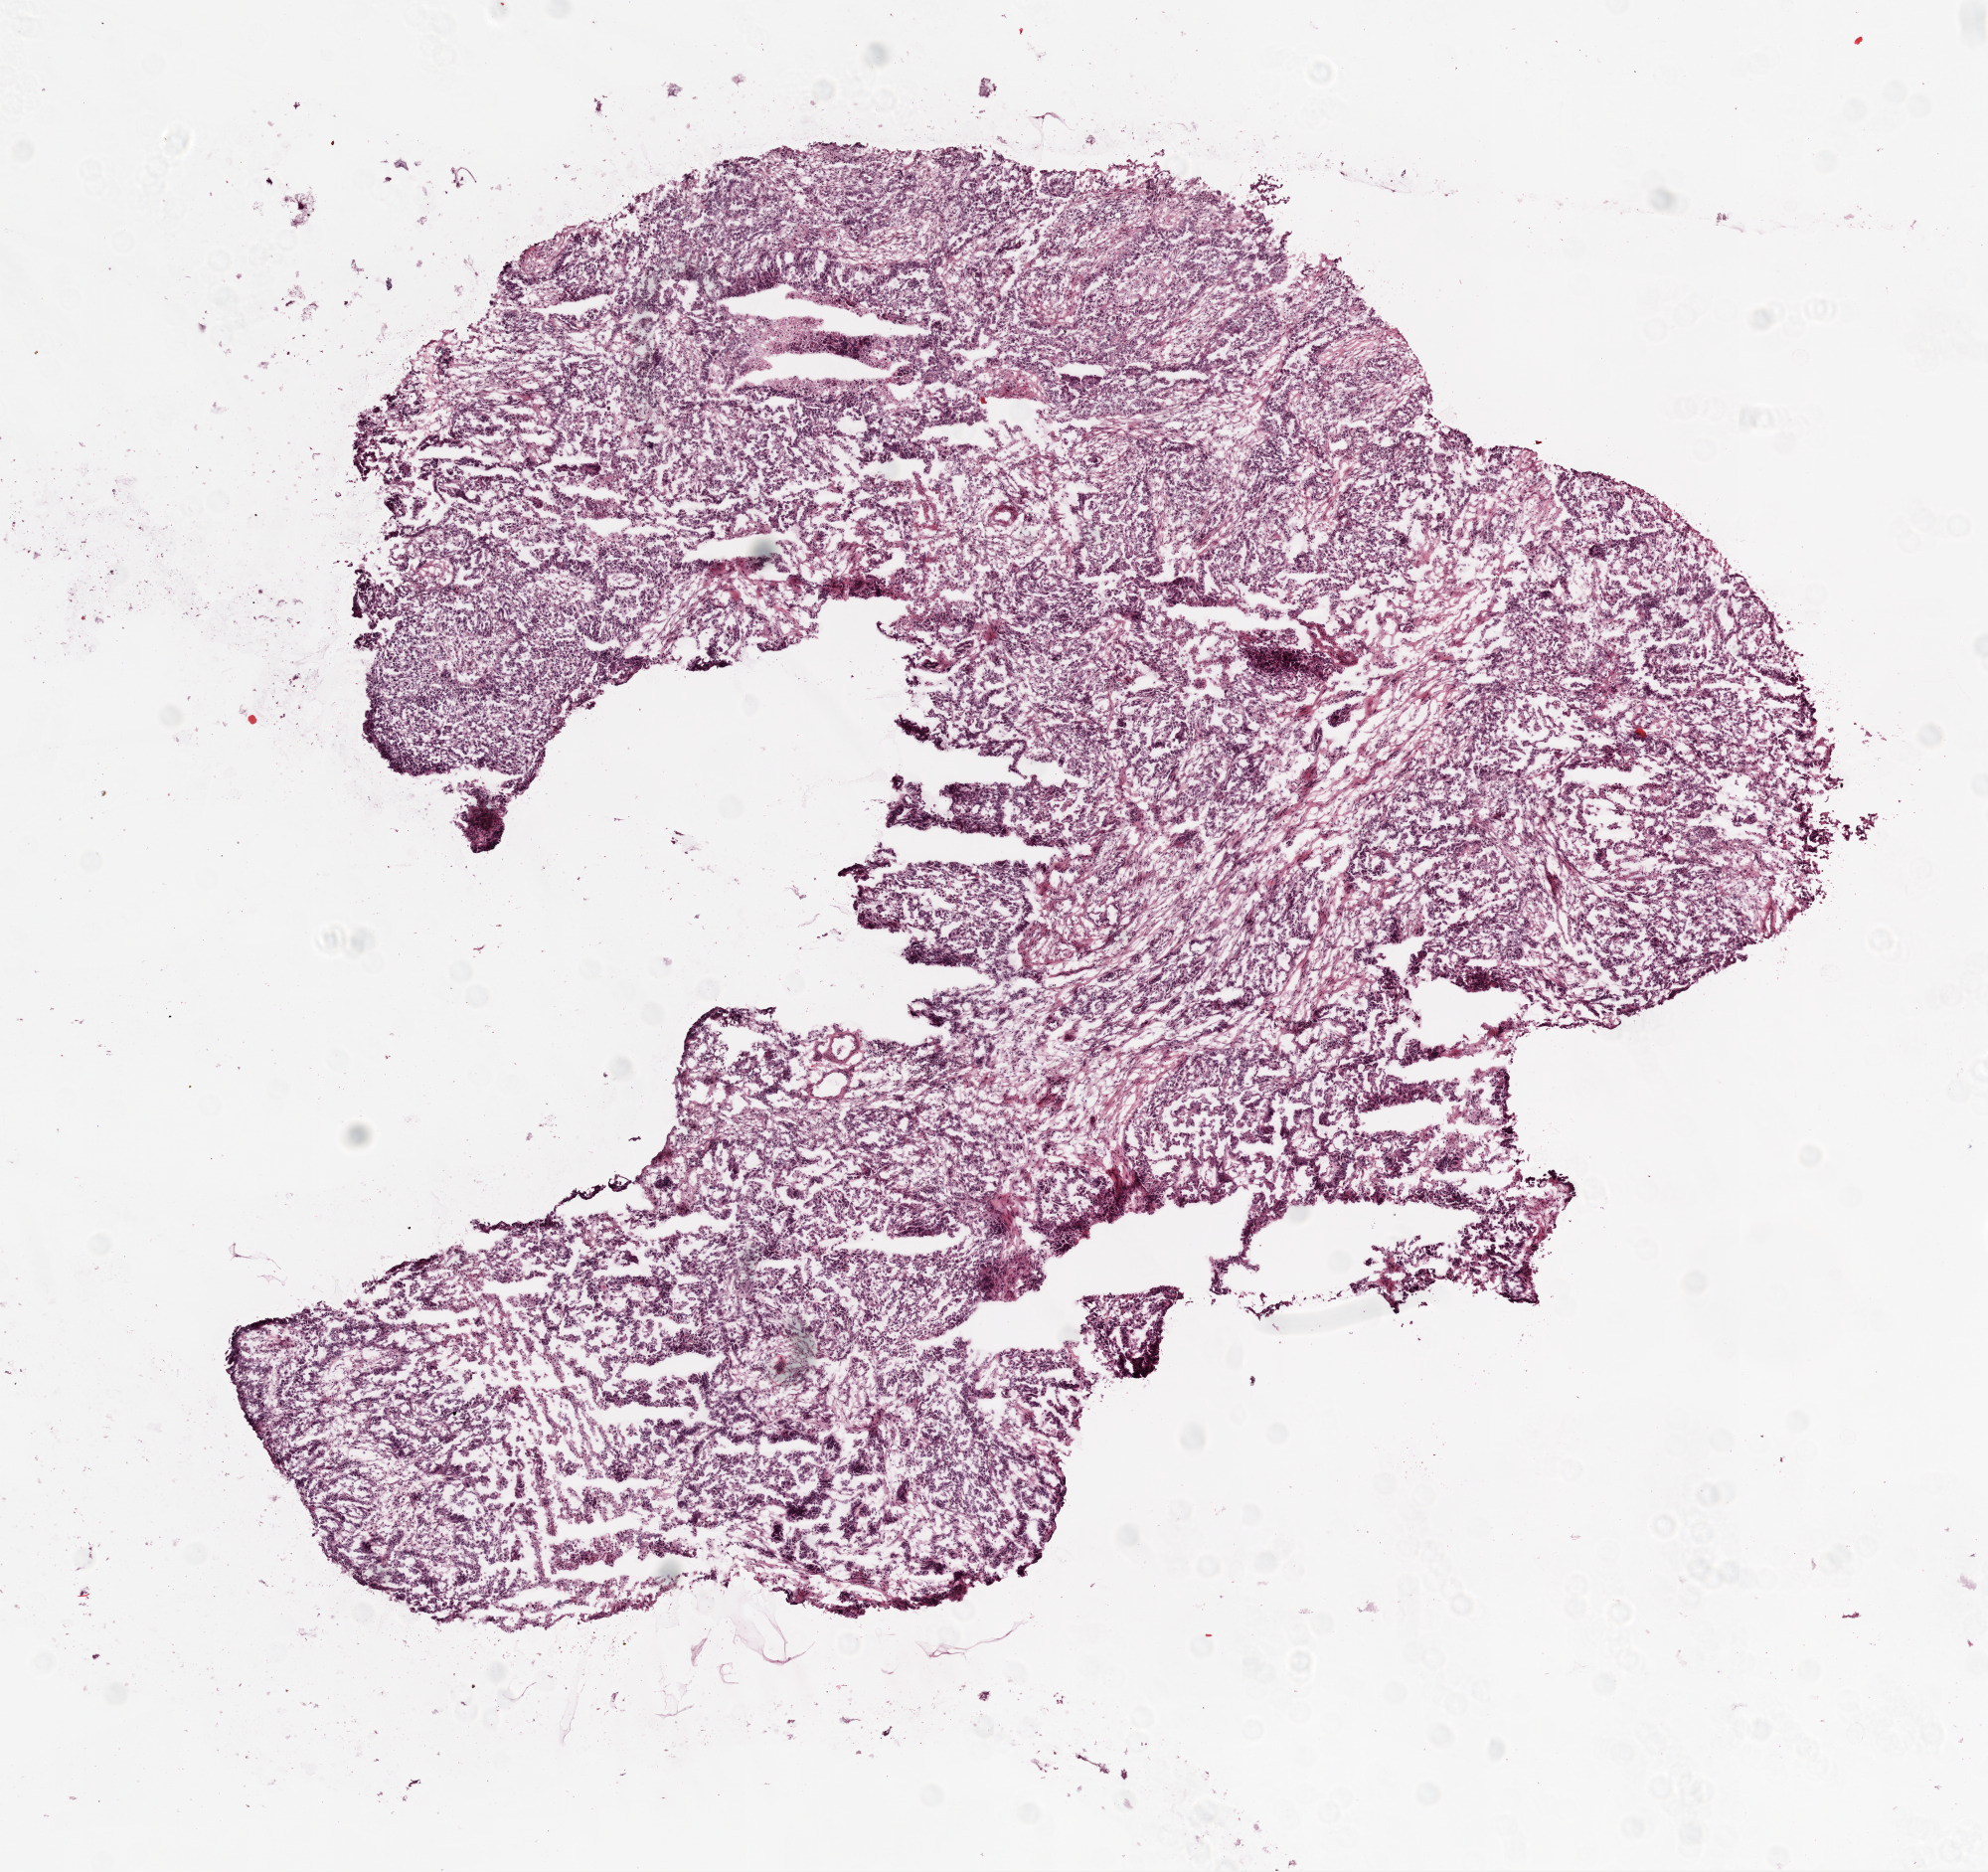
H&E-stained whole-slide image, whole scanned area (about 8.0 x 7.6 mm, acquisition: 20x scan) shown as a low-resolution overview; frozen section from the top of the tissue portion; ovary, primary tumour sample. Female patient; age at initial diagnosis 49 years. Histologic grade: G2 (moderately differentiated). Composition of this section per pathologist review: tumour cells 85%, tumour nuclei 85%, normal cells 0%, stromal cells 12%, necrosis 3%. Inflammatory infiltration, as recorded: lymphocyte infiltration 5%, monocyte infiltration 3%.
Laterality: bilateral. FIGO stage: IIIC. Diagnosis: Serous cystadenocarcinoma, NOS.